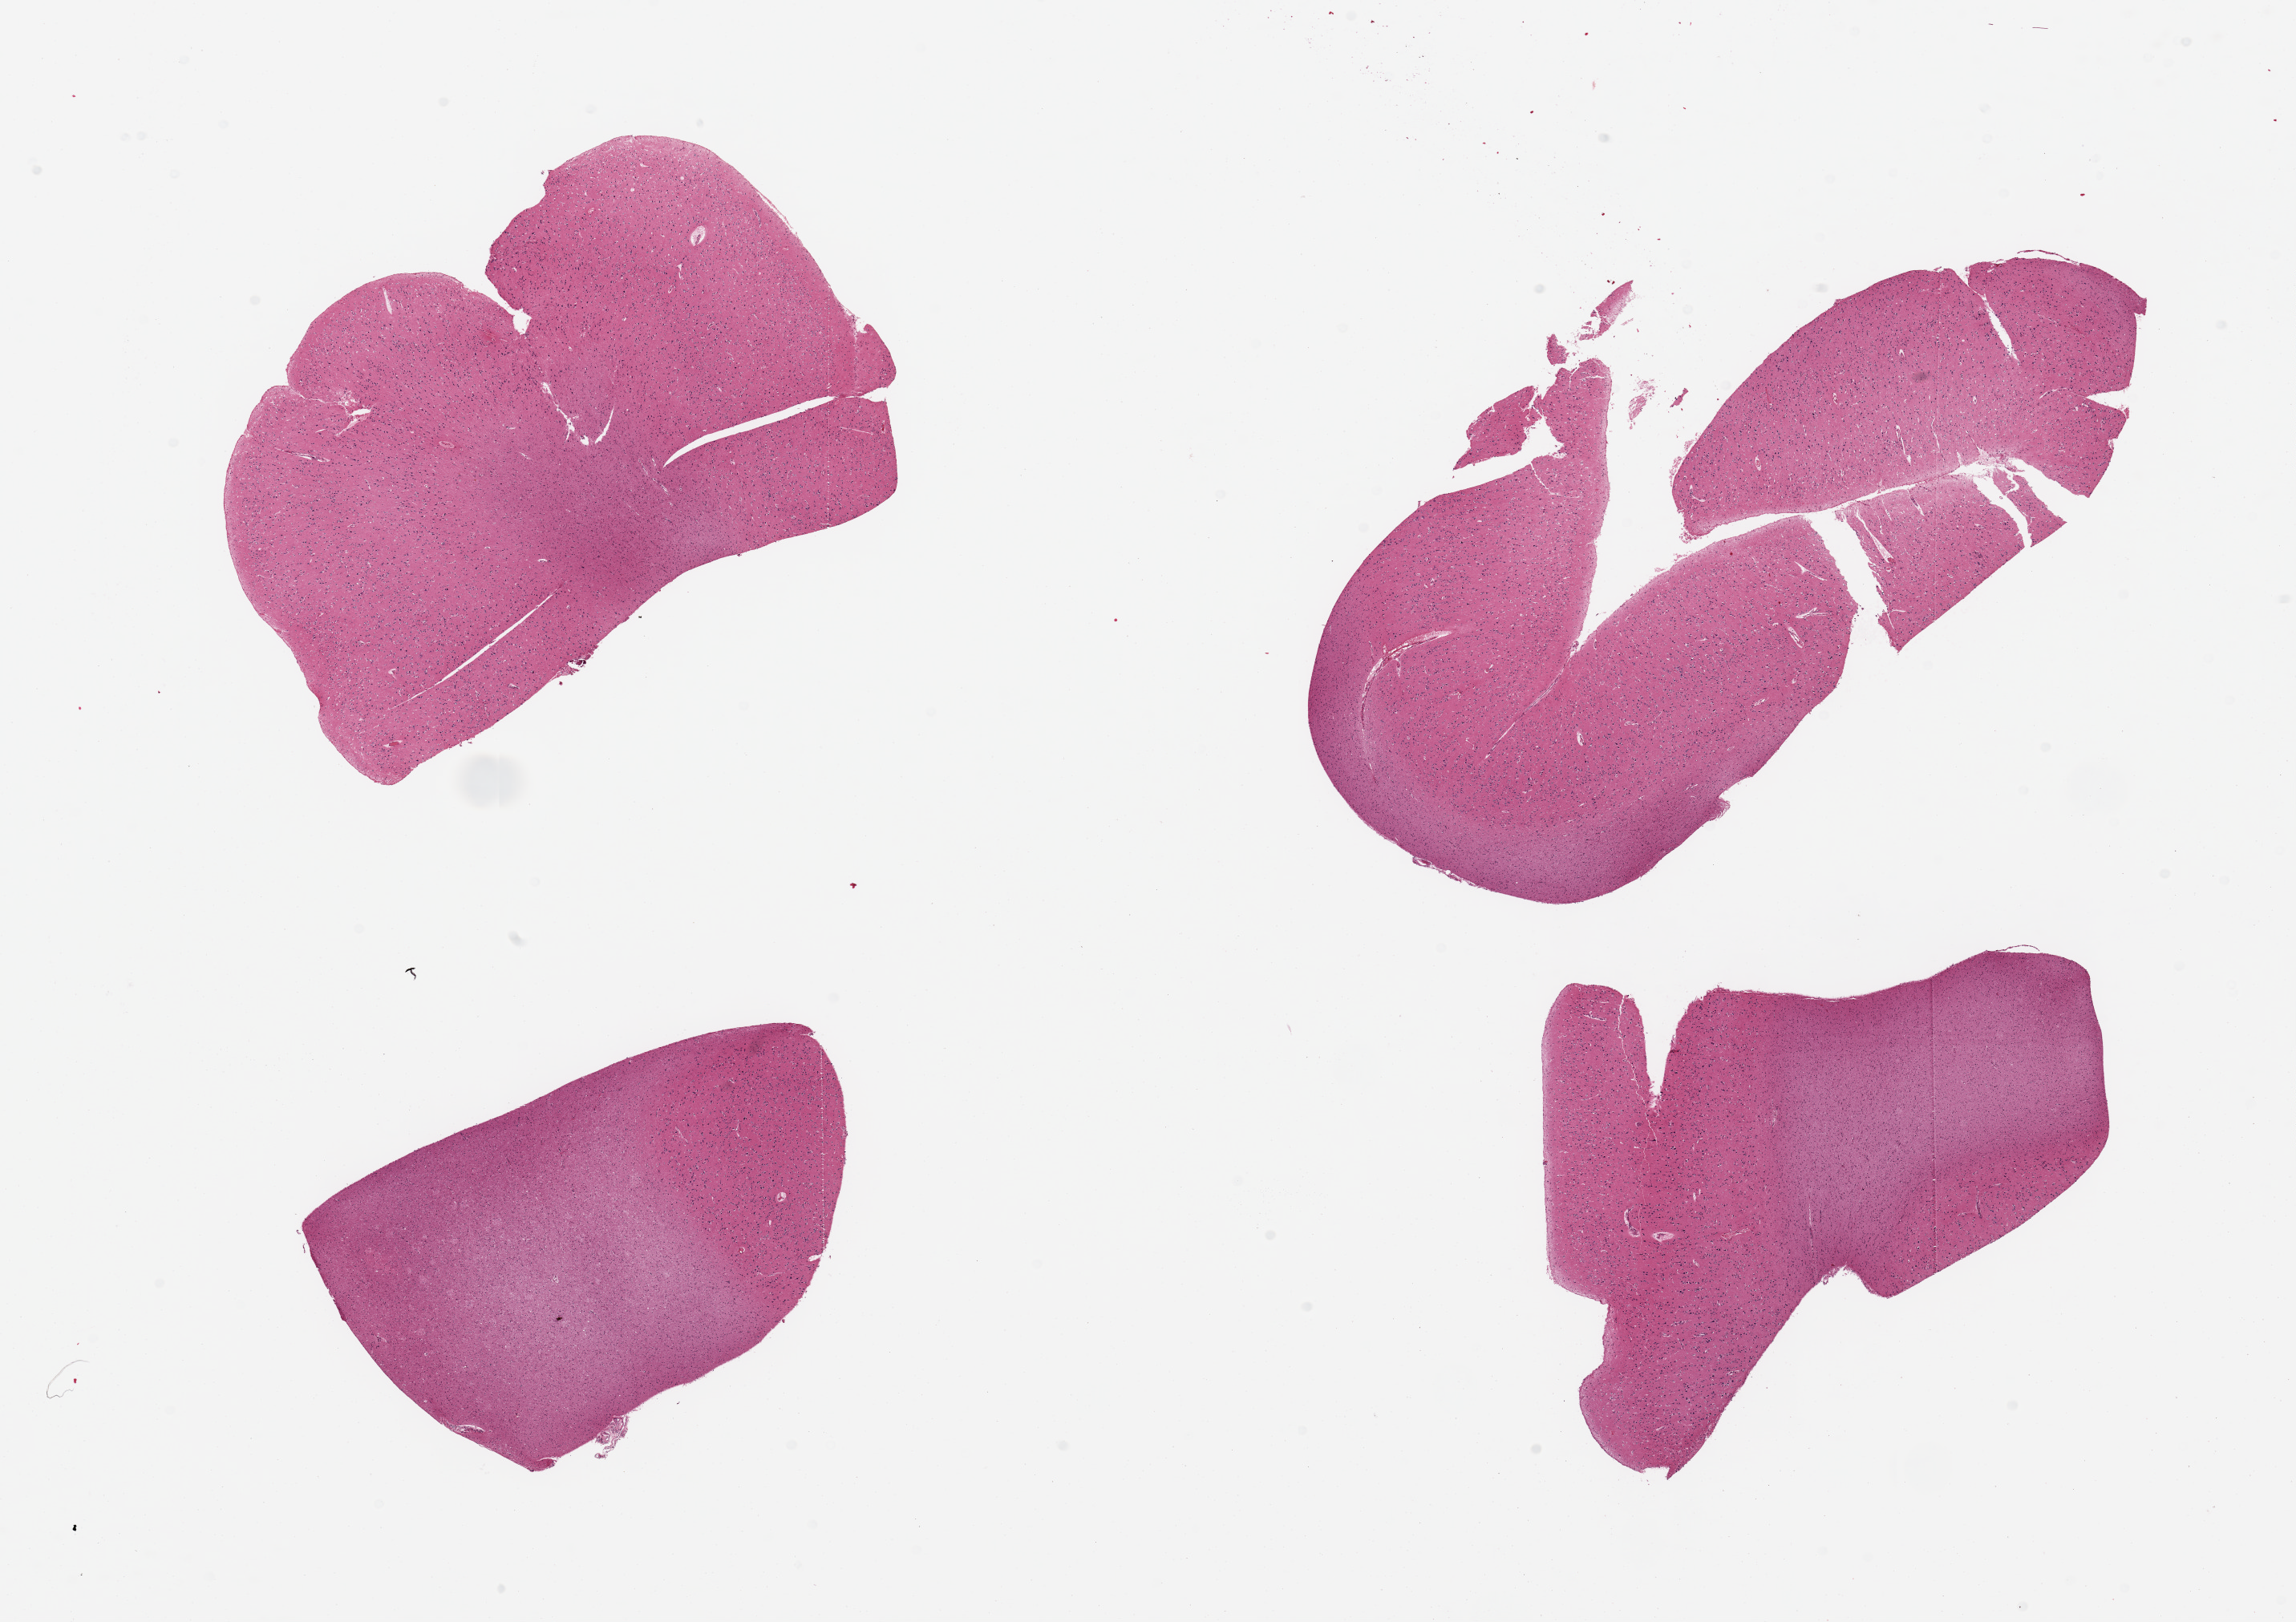
Whole-slide image, H&E stain, brightfield, a low-resolution overview of the entire scanned area, about 22.6 x 16.0 mm; PAXgene-fixed, paraffin-embedded tissue; sampled site (target tissue): cerebral cortex; tissue donor sample. Donor: male.
Pathologist's review note for this sample: 4 pieces; 2 smaller pieces have admixture with white matter.